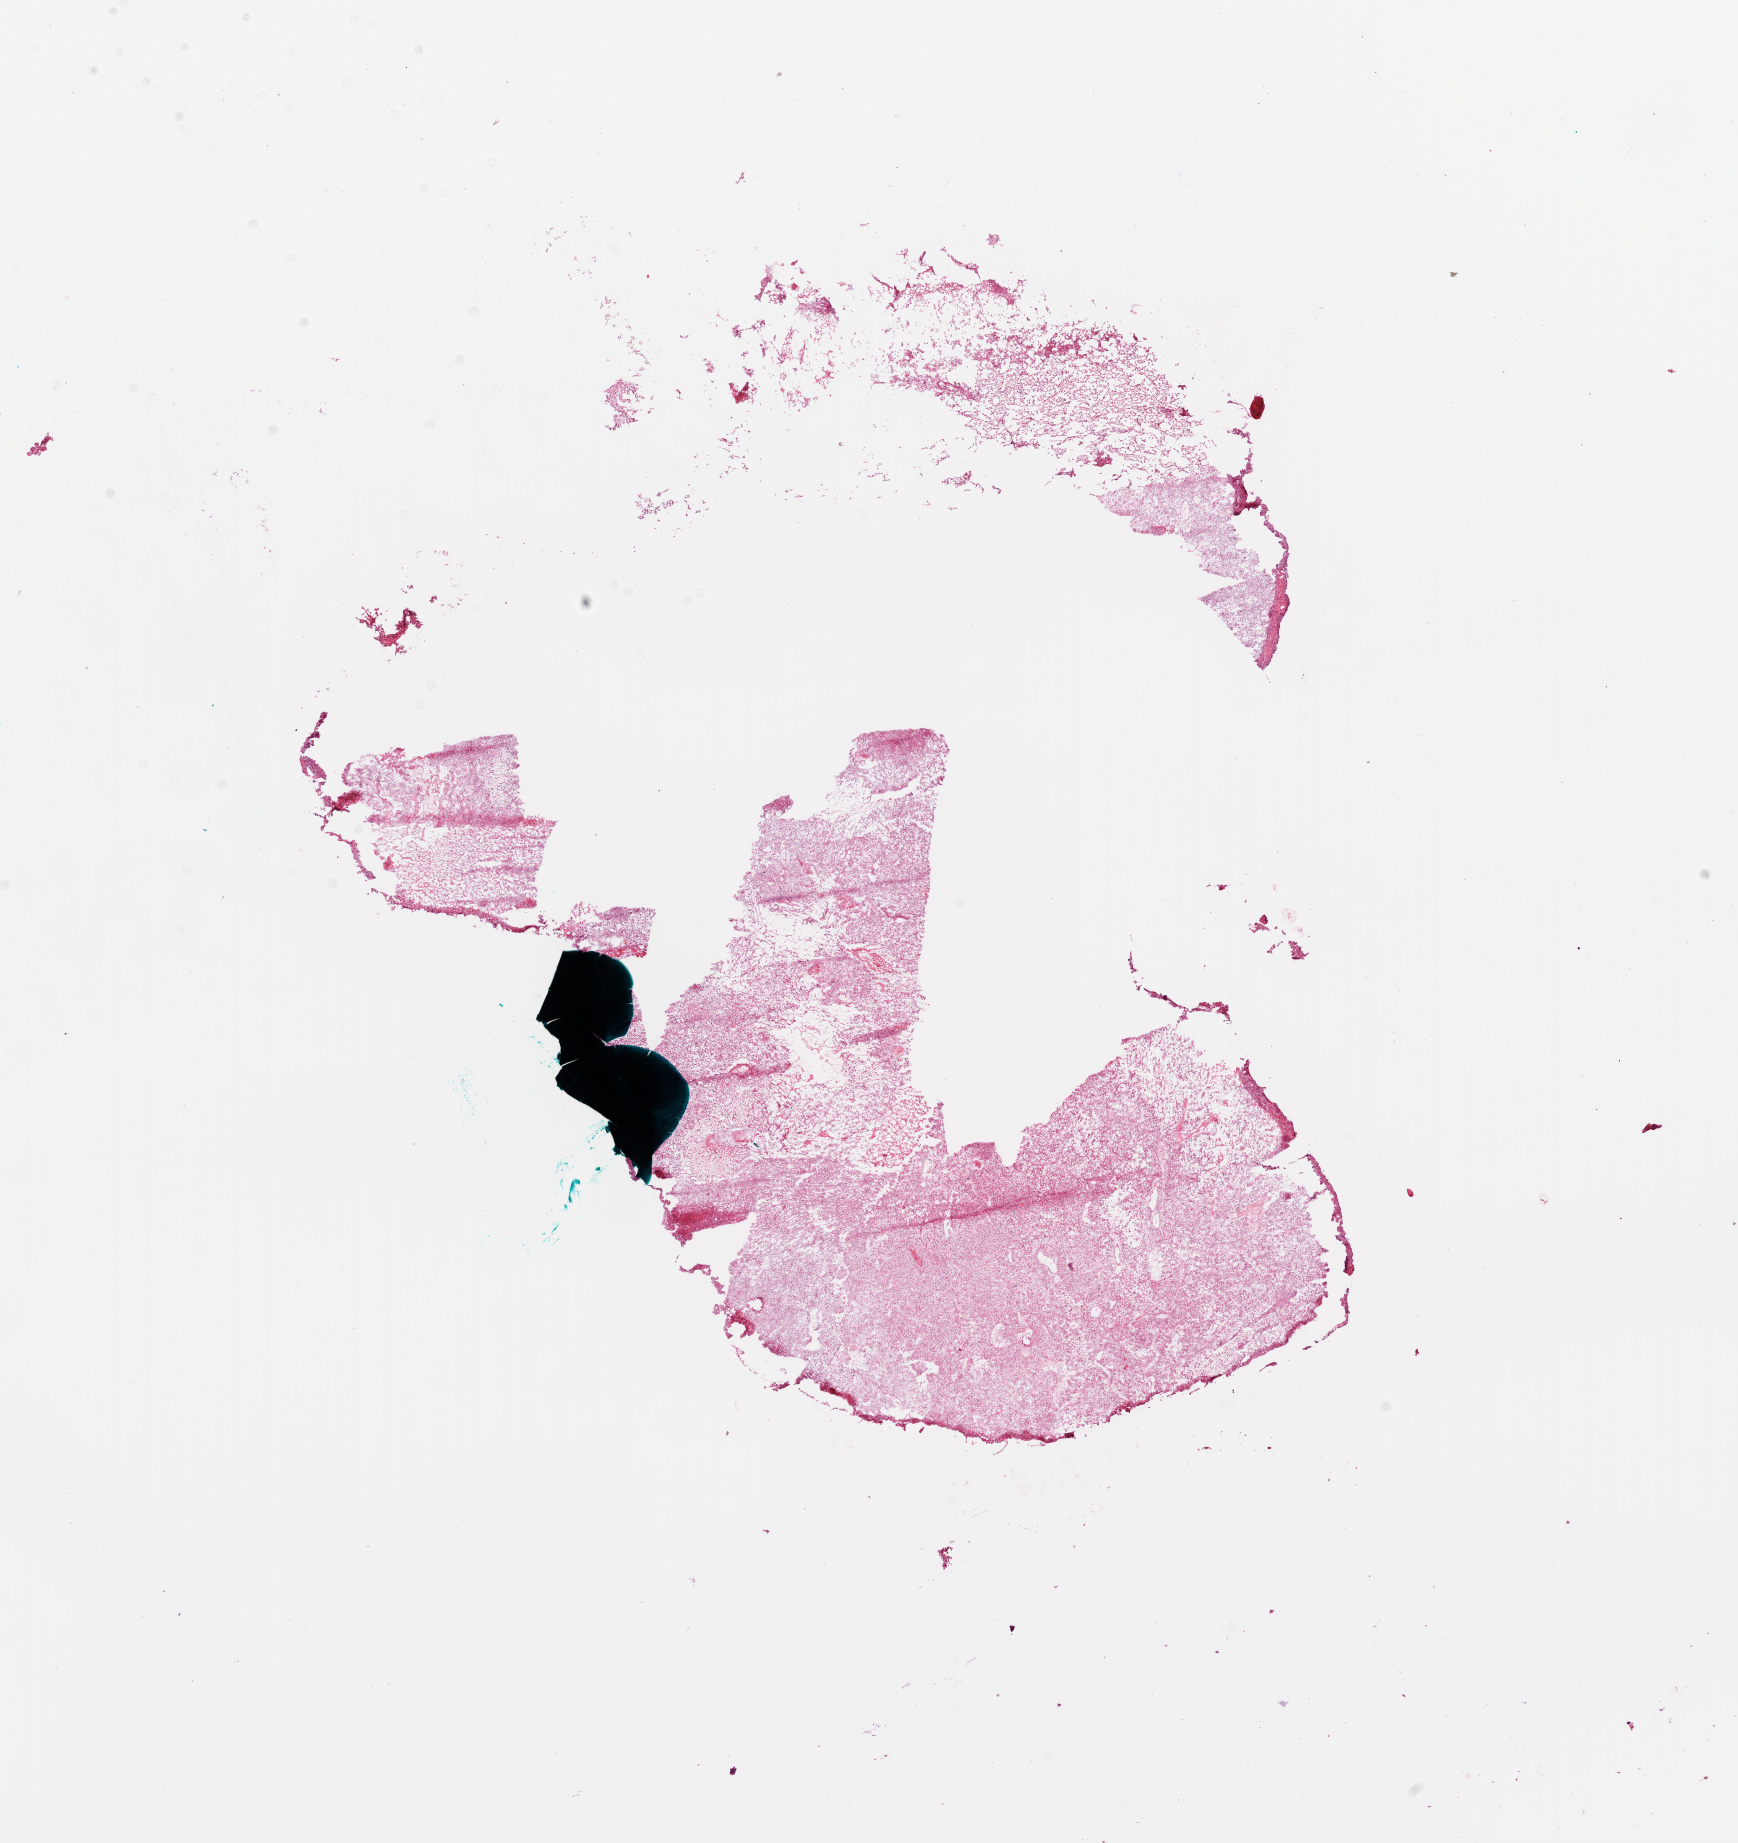
H&E whole-slide image — low-resolution overview of the scanned area, about 14.0 x 14.9 mm, frozen section from the bottom of the tissue portion, sample: primary tumour, brain. Female patient; age at initial diagnosis 66 years. Slide review estimates, as recorded: tumour cells 80%, tumour nuclei 100%, normal cells 0%, stromal cells 0%, necrosis 20%.
* diagnosis: Glioblastoma